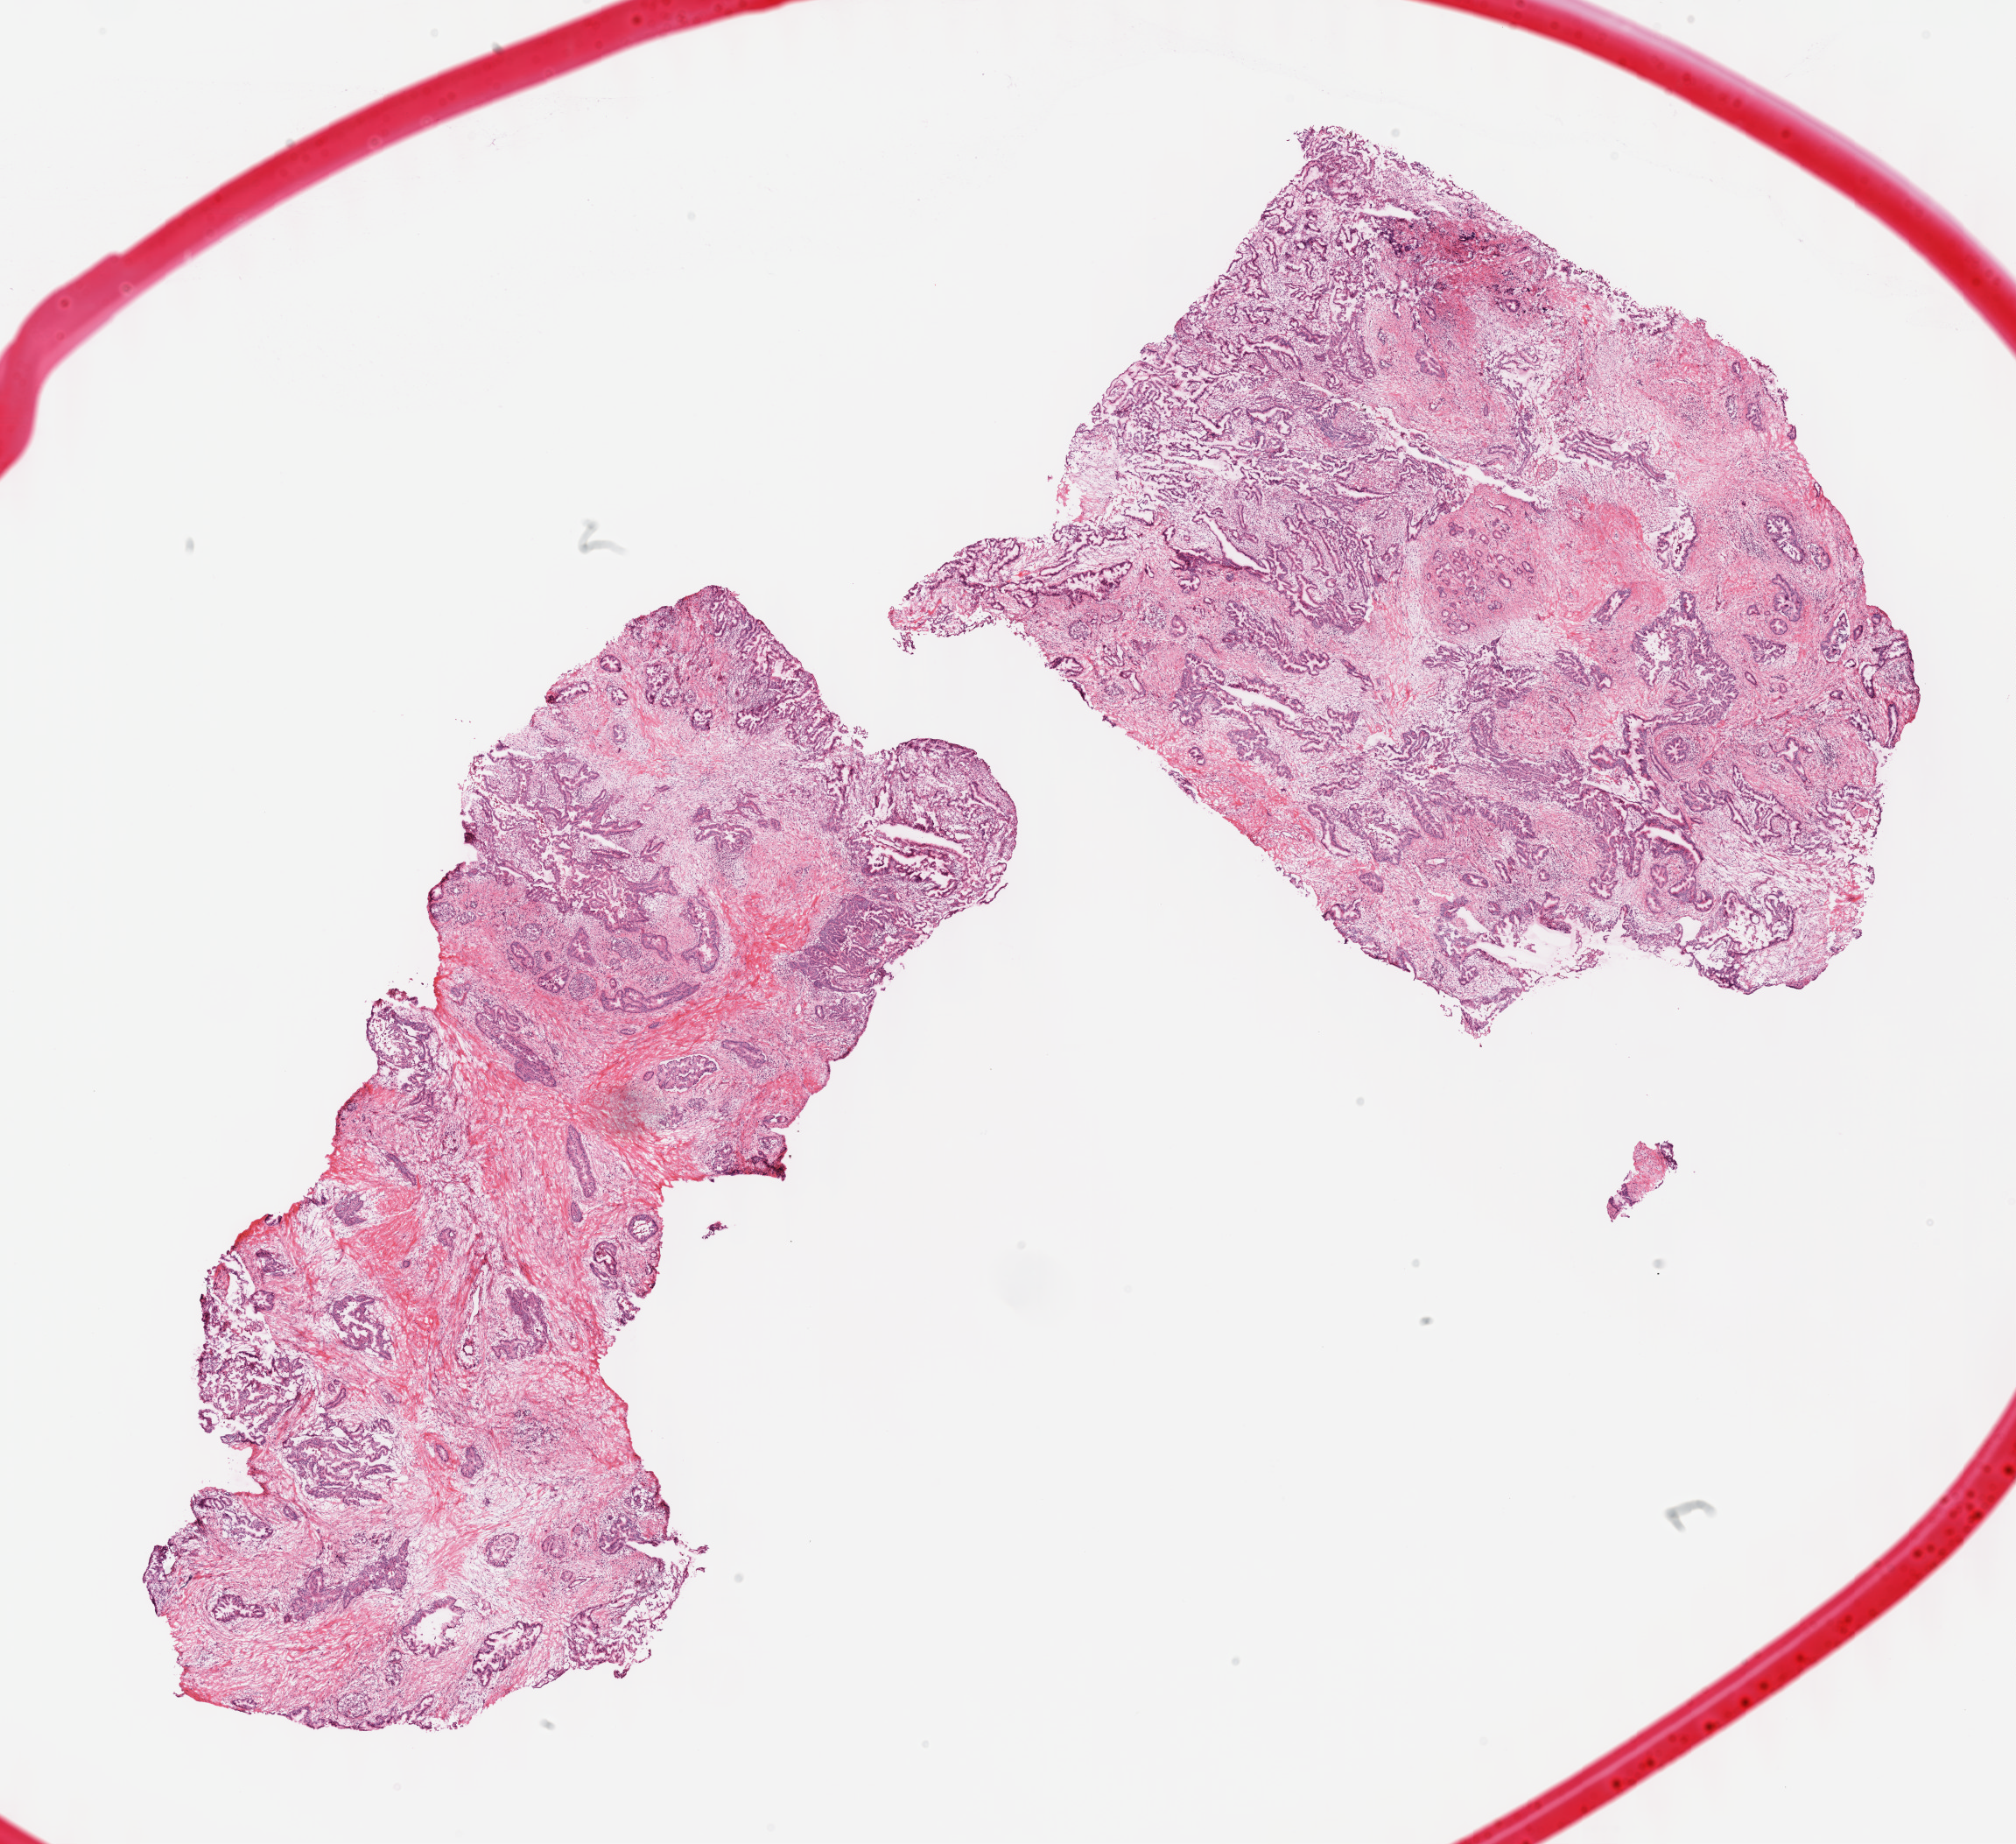
H&E-stained whole-slide image, low-resolution overview of the scanned area, about 18.6 x 17.0 mm (acquisition: 40x scan). FFPE section. Sample: primary tumour, pancreas. Female patient; age at initial diagnosis 41 years. Histologic grade: G2 (moderately differentiated).
AJCC pathologic stage: IIA (7th edition). Histologic diagnosis: Infiltrating duct carcinoma, NOS (head of pancreas). Lymph nodes positive (case pathology): 0 of 12 examined.